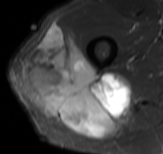
MRI of an extremity soft-tissue mass, one axial slice. Slice 52 of 61 in the series (ordered by position). STIR. MR volume resampled by the dataset authors to the PET/CT grid (not the native acquisition matrix). 163 × 154 image matrix, field of view 159 × 150 mm. Male patient. From the clinical record (not read from this slice): histological type: poorly differentiated synovial sarcoma; grade: high; site of the primary tumour: right buttock.
Annotated regions visible in this slice (expert contour drawn on MRI and transferred to this co-registered scan by the dataset authors):
- gross tumour volume including surrounding oedema: bounding box [x1, y1, x2, y2] px = [21, 23, 129, 138]
- gross tumour volume (mass): [21, 23, 129, 138]